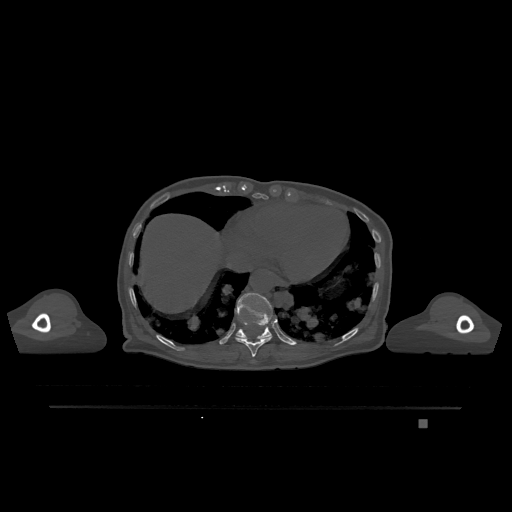
CT including the spine, one axial slice. Slice 620 of 1317 in the series (ordered by position). Bone window (W 1800 / L 400 HU). 512 × 512 image matrix, field of view 500 × 500 mm. Patient: female, 74 years. From the clinical record (not read from this slice): primary cancer: lung; vertebrae with lytic lesions (as recorded): T1, T4, T5, T6, L4, L5.
Annotated regions visible in this slice (semi-automatic segmentation, software-assisted and operator-edited):
- T10 vertebra: bounding box (x1, y1, x2, y2) in pixels: (235, 336, 272, 357)
- T11 vertebra: (235, 293, 276, 339)